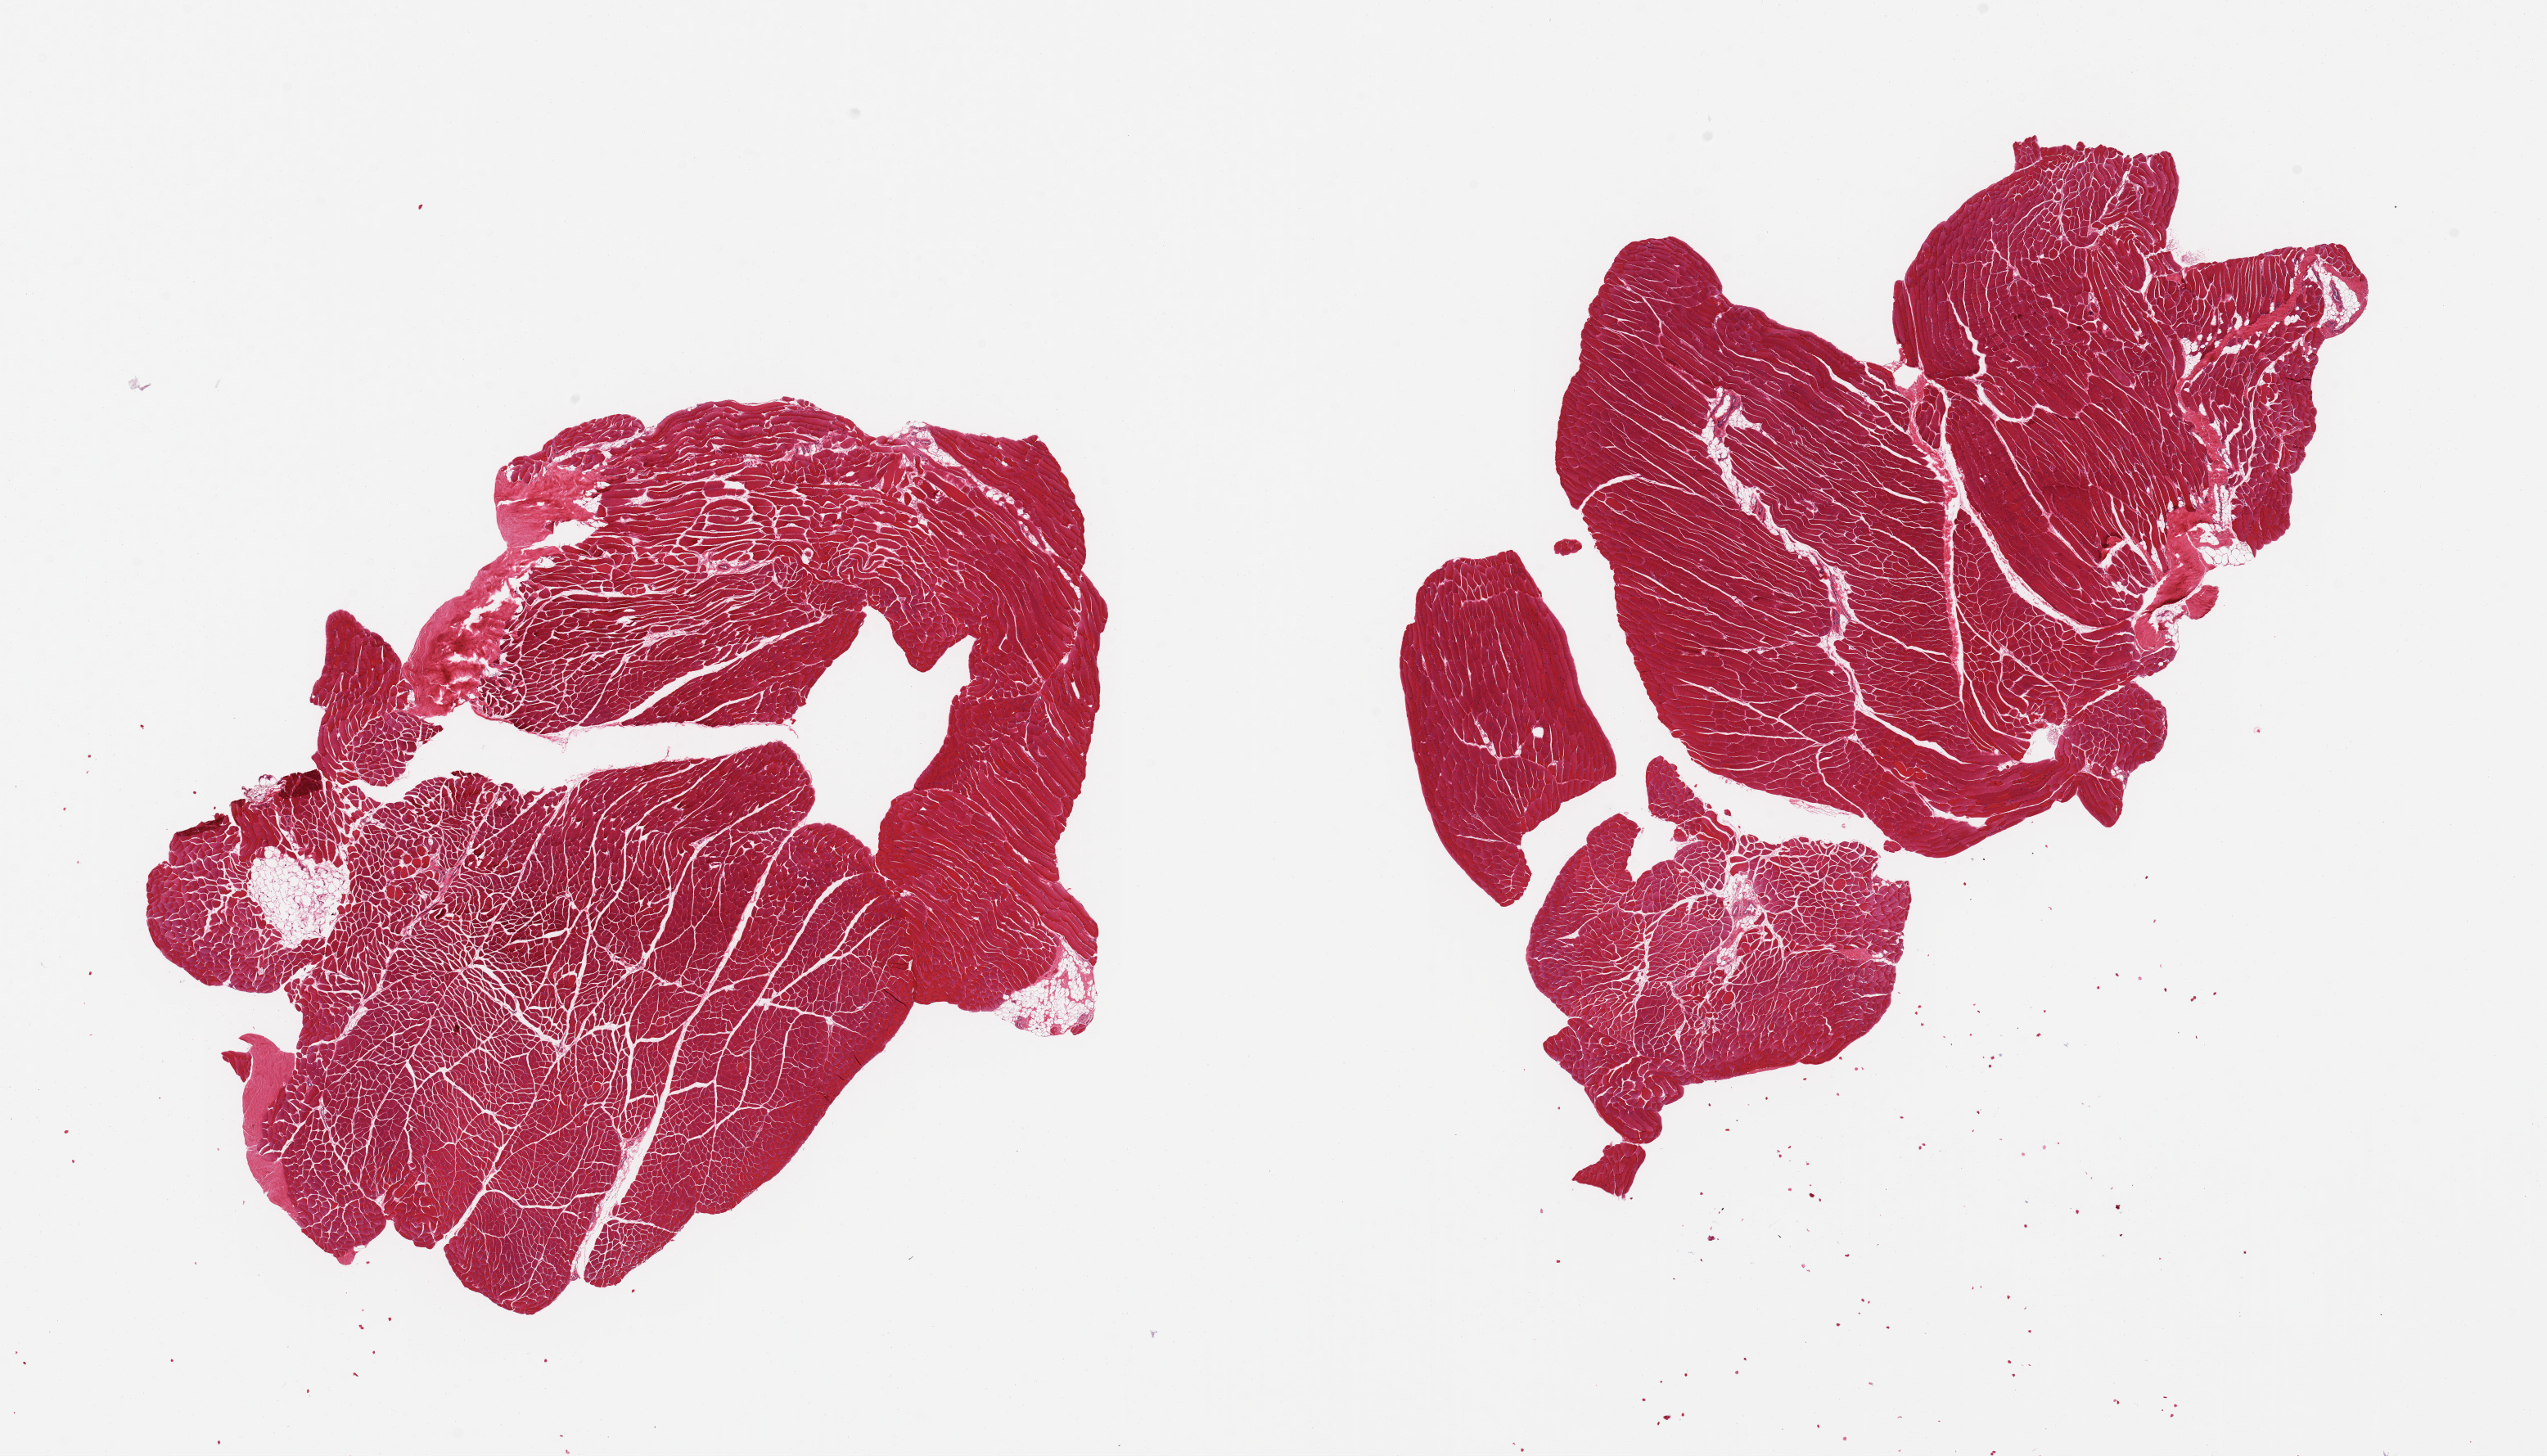
Digitized hematoxylin and eosin (H&E)-stained section, brightfield — shown as a low-resolution overview of the whole scanned area (about 24.6 x 14.1 mm, acquisition: 20x scan). PAXgene-fixed paraffin-embedded (PFPE) section. Target tissue: skeletal muscle. Donor tissue sample. Male donor.
Reviewer comment on this tissue sample: 2 pieces; skeletal muscle with small component of fat/tendon.